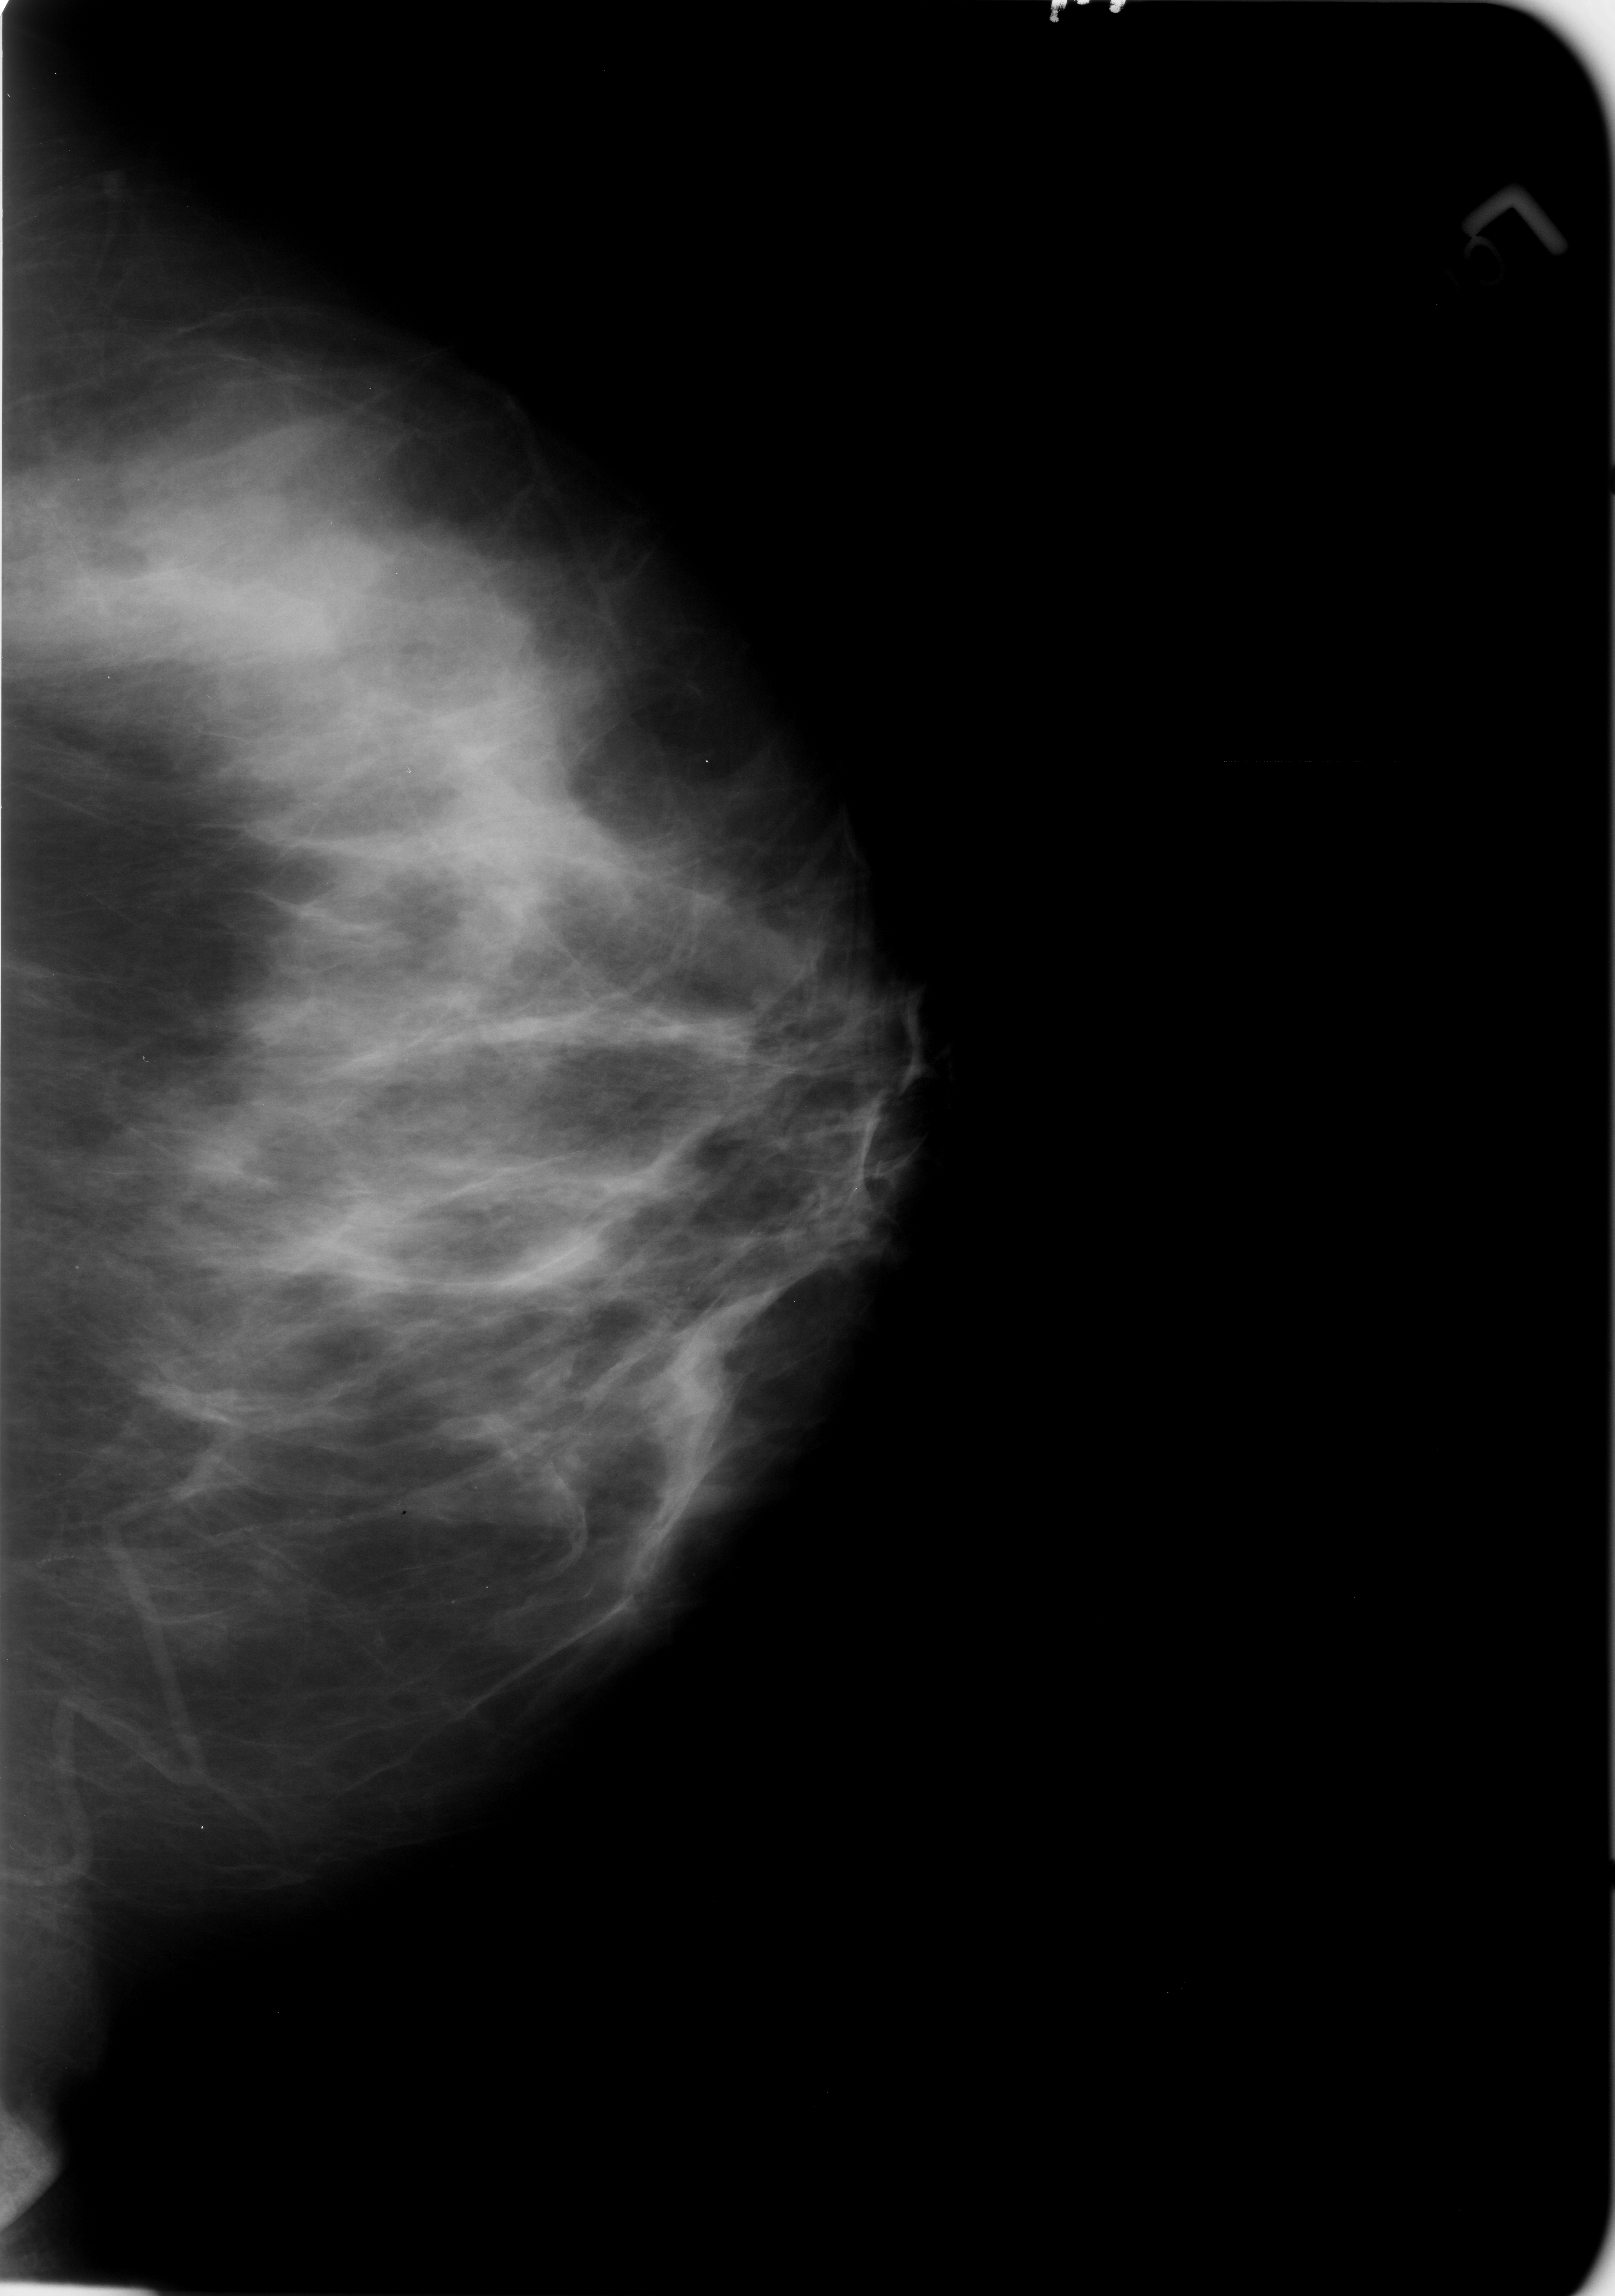
Mammogram (digitized film); left breast; CC view; breast composition: heterogeneously dense (BI-RADS density category 3 of 4).
Marked findings (only marked abnormalities are described; nothing is implied about the rest of the image): calcifications, morphology vascular; BI-RADS assessment category 2; subtlety rating 3 on a 1 (subtle) to 5 (obvious) scale; benign; no additional work-up was recommended (benign without callback).